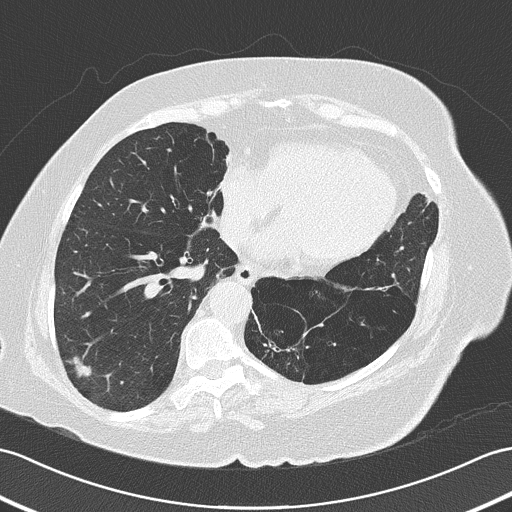
Low-dose screening chest CT, axial slice, baseline annual screen, lung window (W 1500 / L -600 HU), 2 mm slice thickness, slice 98 of 161 in the series, 512 × 512 image matrix. Female participant, aged 73 years at enrolment.
Expert-annotated lung lesion, bounding box (x1, y1, x2, y2) in pixels: (55, 339, 101, 387). The screening reader recorded 4 non-calcified nodules or masses ≥4 mm on this exam; which of them this box marks is not recorded. Official screen result: positive, change unspecified: nodule(s) >= 4 mm or enlarging nodule(s), mass(es), or other non-specific abnormalities suspicious for lung cancer. Participant outcome: lung cancer diagnosed 50 days after this screen — adenocarcinoma, NOS, right lower lobe, poorly differentiated (G3), stage IB (AJCC 6th edition), 17 mm at pathology.